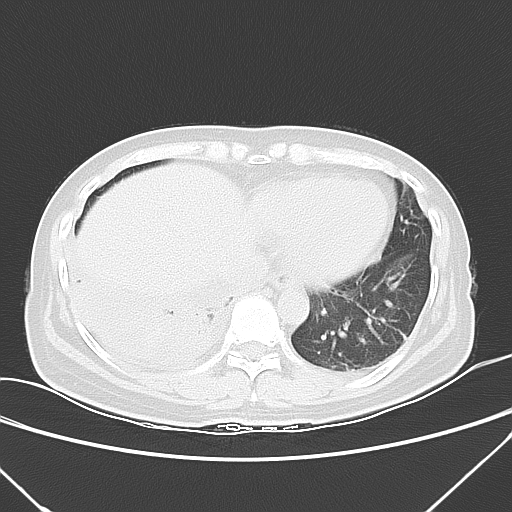
Chest CT, one axial slice. Position 12 of 53 along the scan axis. 120 kVp. Lung window (W 1500 / L -600 HU). 512 × 512 image matrix, field of view 337 × 337 mm. Patient: female, 42 years. Case-level facts recorded for this patient, not image findings: clinical TNM (as recorded): T3 N0 M1c.
Structures marked on this image (rectangle marked by the reading radiologist):
- lung tumour (recorded histology: adenocarcinoma): bounding box [x1, y1, x2, y2] px = [81, 294, 215, 377]